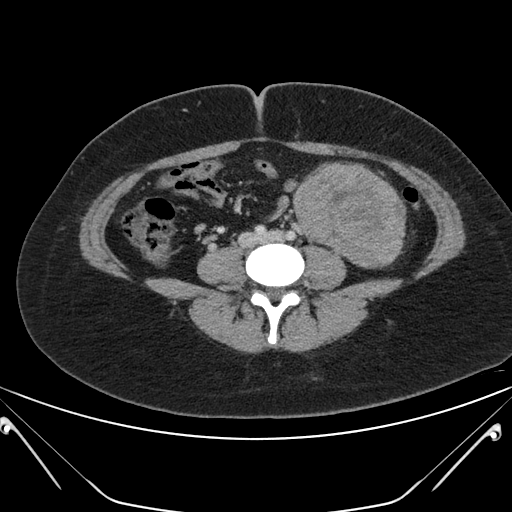
Contrast-enhanced abdominal CT, one axial slice; slice 76 of 168 in the series (ordered by position); 120 kVp; intravenous contrast given; soft-tissue window (W 400 / L 40 HU); 512 × 512 image matrix, field of view 394 × 394 mm. Female patient, age 26 years. From the clinical record (not read from this slice): diagnosis: adrenocortical carcinoma; tumour side: left adrenal; tumour size at pathology: 28 cm; Ki-67 index: 20 %; stage (as recorded): 2.
Annotated regions visible in this slice (semi-automatically segmented with operator editing):
- mass: bounding box <293,164,405,264> (left, top, right, bottom; pixels)